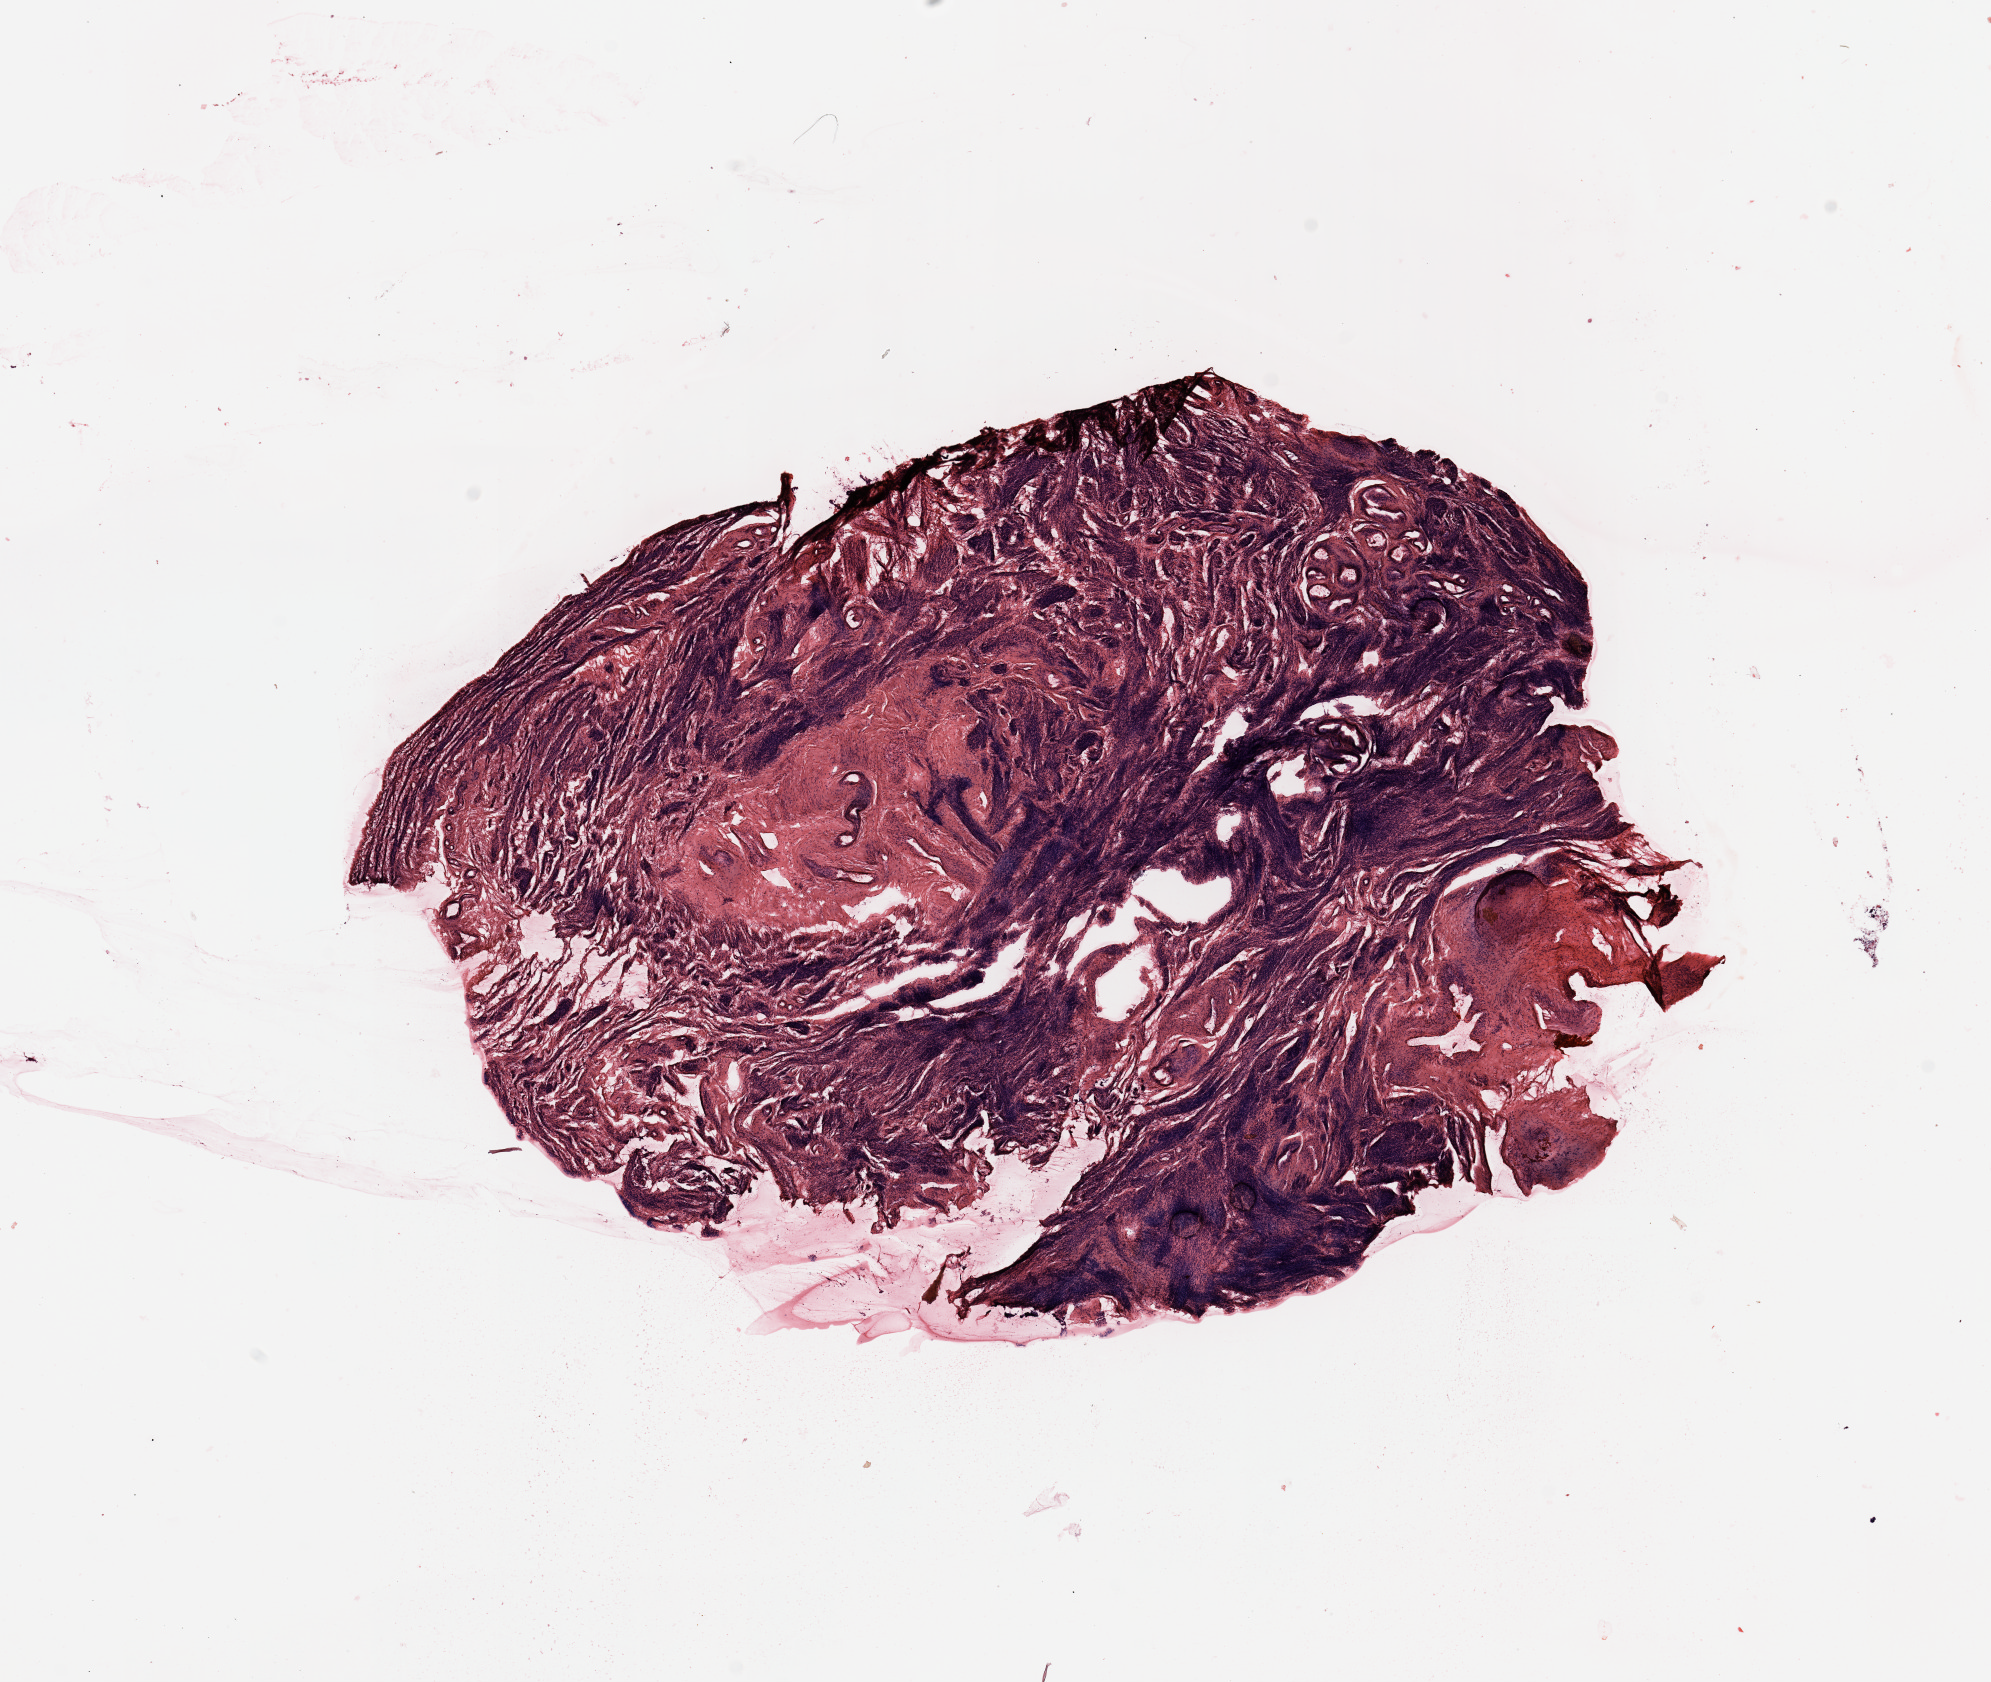
Digitized Hematoxylin and eosin (H&E) stained tissue section (whole slide), shown as a low-resolution overview of the whole scanned area (about 15.8 x 13.3 mm, acquisition: 20x scan); uterus, normal (non-tumour) tissue. Female, 70 y/o.
This section: normal (non-tumour) tissue from the same patient. Patient diagnosis: Endometrioid adenocarcinoma, NOS.